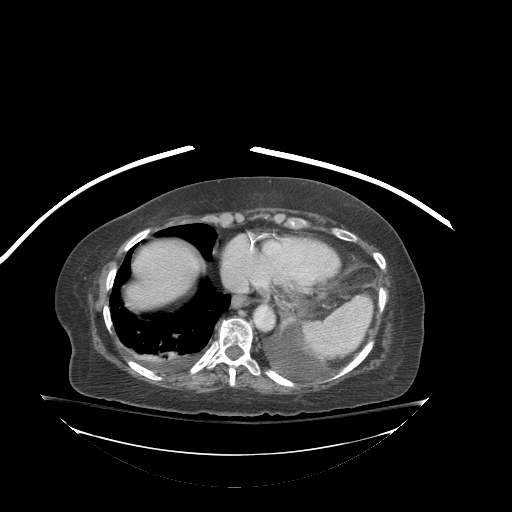
Contrast-enhanced abdominal CT (liver protocol), one axial slice; position 78 of 81 along the scan axis; reconstruction kernel STANDARD; 140 kVp; soft-tissue window (W 400 / L 40 HU); 2.5 mm slice thickness; 512 × 512 image matrix, field of view 500 × 500 mm. Case-level facts recorded for this patient, not image findings: diagnosis: hepatocellular carcinoma (patient treated with transarterial chemoembolisation; whether this scan precedes or follows treatment is not stated here); TNM stage (as recorded): Stage-I; Child-Pugh class: B; tumour differentiation: well-moderately differentiated.
Annotated regions visible in this slice (semi-automatically segmented with operator editing):
- abdominal aorta: bounding box <255,306,273,328> (left, top, right, bottom; pixels)
- liver parenchyma outside the tumour (the mass and vessels are separate outlines, so this box may not span the whole liver): <126,240,202,308>